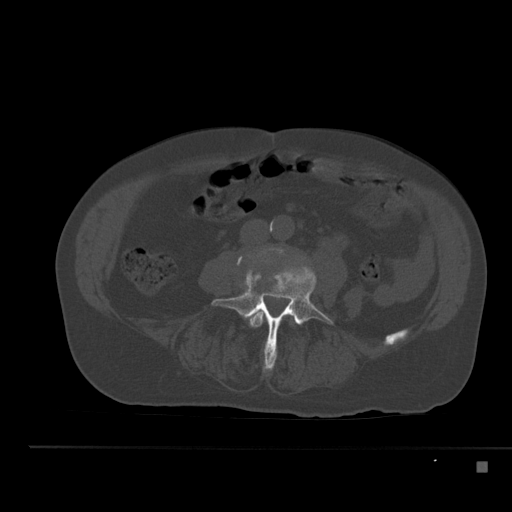
CT including the spine, one axial slice. Slice 147 of 517 in the series (ordered by position). 120 kVp. Bone window (W 1800 / L 400 HU). 1.5 mm slice thickness. 512 × 512 image matrix, field of view 408 × 408 mm. Patient: male, 70 years. From the clinical record (not read from this slice): primary cancer: renal.
Structures marked on this image (semi-automatically segmented with operator editing):
- L3 vertebra: bounding box [x1, y1, x2, y2] px = [250, 310, 294, 352]
- L4 vertebra: [212, 256, 334, 370]